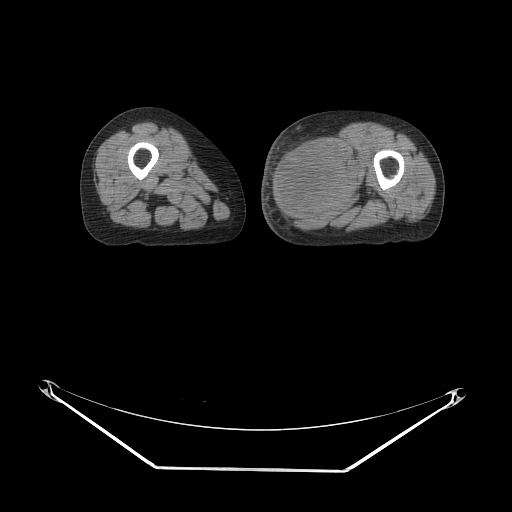
CT of an extremity soft-tissue mass (from a PET/CT study), one axial slice; slice 25 of 91 in the series (ordered by position); soft-tissue window (W 400 / L 40 HU); 512 × 512 image matrix. Female patient. Case-level facts recorded for this patient, not image findings: histological type: pleomorphic leiomyosarcoma; grade: high; site of the primary tumour: left thigh.
Outlined on this slice (expert contour drawn on MRI and transferred to this co-registered scan by the dataset authors):
- gross tumour volume including surrounding oedema: bounding box <270,135,357,218> (left, top, right, bottom; pixels)
- gross tumour volume (mass): <270,139,355,218>